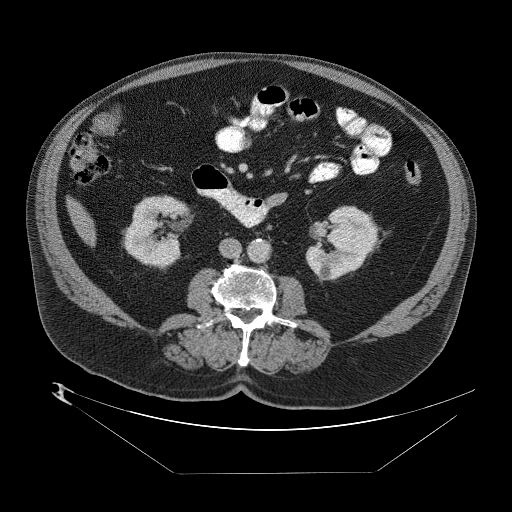
Contrast-enhanced abdominal CT (liver protocol), one axial slice. Position 5 of 89 along the scan axis. 140 kVp. One of 2 acquisitions stored at this slice position. Soft-tissue window (W 400 / L 40 HU). 512 × 512 image matrix. From the clinical record (not read from this slice): diagnosis: hepatocellular carcinoma (patient treated with transarterial chemoembolisation; whether this scan precedes or follows treatment is not stated here); TNM stage (as recorded): Stage-II; Child-Pugh class: B.
Annotated regions visible in this slice (semi-automatic segmentation, software-assisted and operator-edited):
- abdominal aorta: bounding box <247,240,270,264> (left, top, right, bottom; pixels)
- liver parenchyma outside the tumour (the mass and vessels are separate outlines, so this box may not span the whole liver): <64,190,94,242>